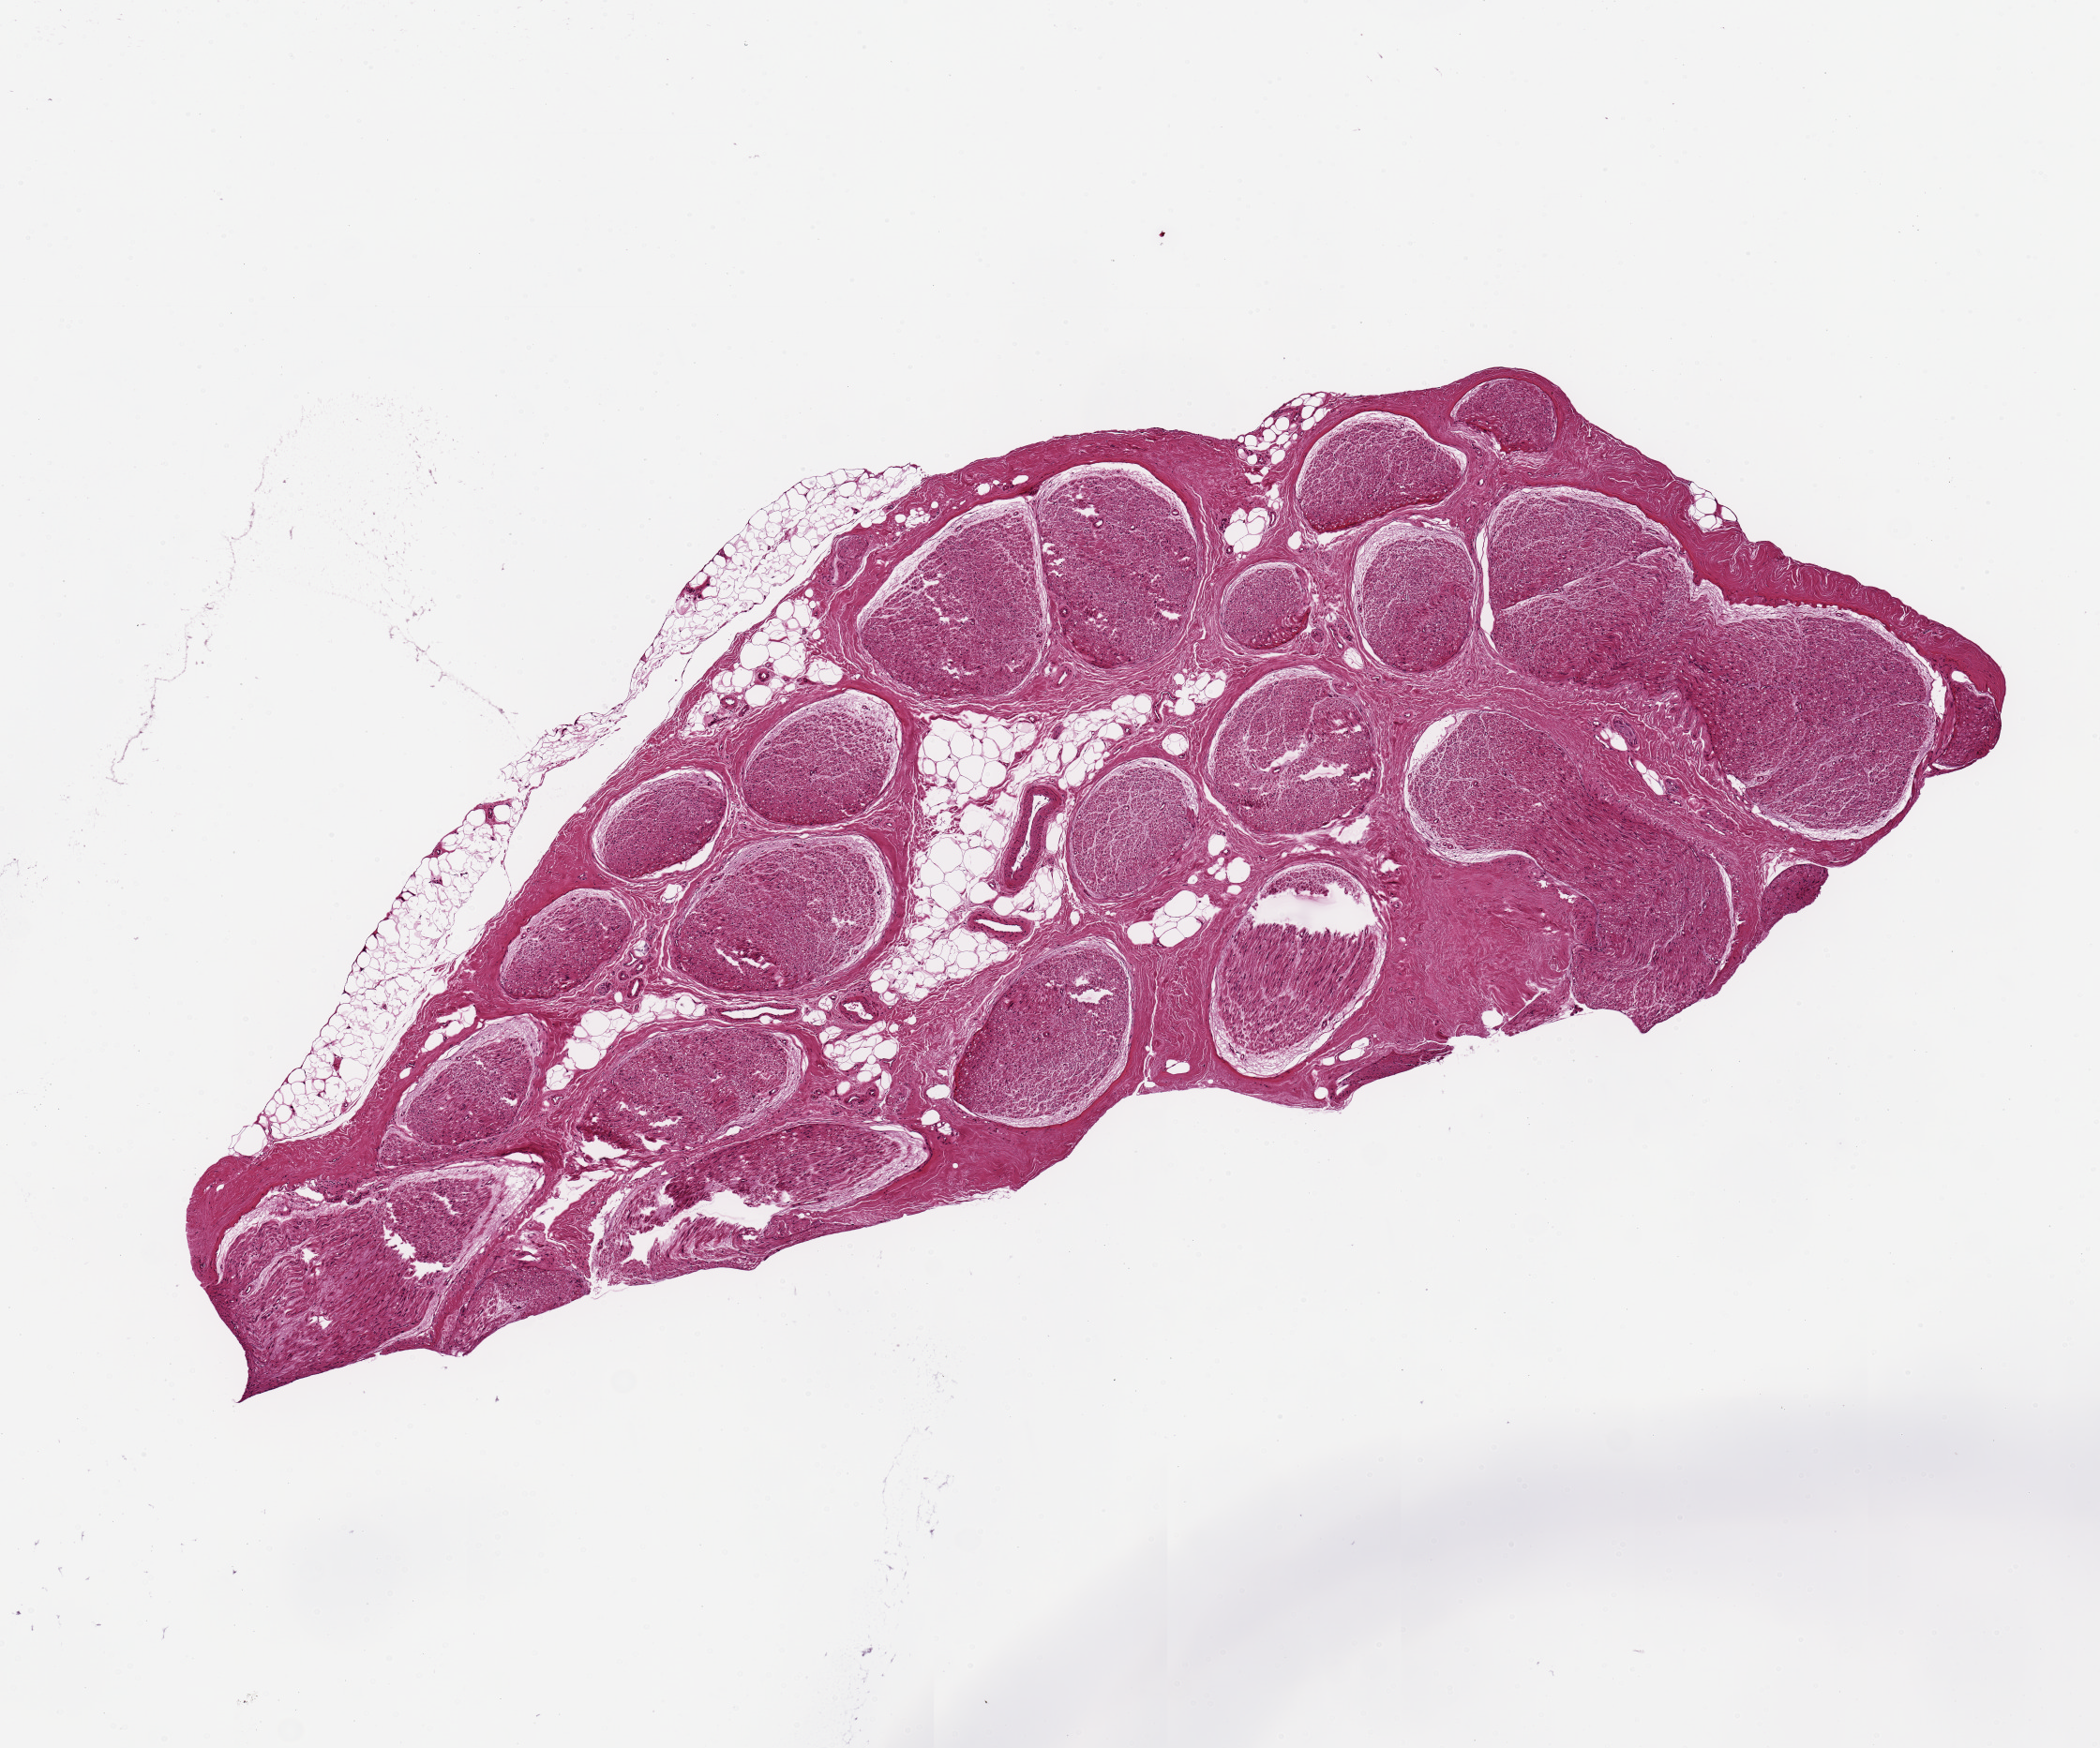
Digitized haematoxylin and eosin-stained section, shown as a low-resolution overview of the whole scanned area (about 8.9 x 7.4 mm, acquisition: 20x scan). PAXgene-fixed paraffin-embedded (PFPE) section. Target tissue: tibial nerve. Donor tissue sample. Male donor.
Review note (as recorded): About 10% fat.